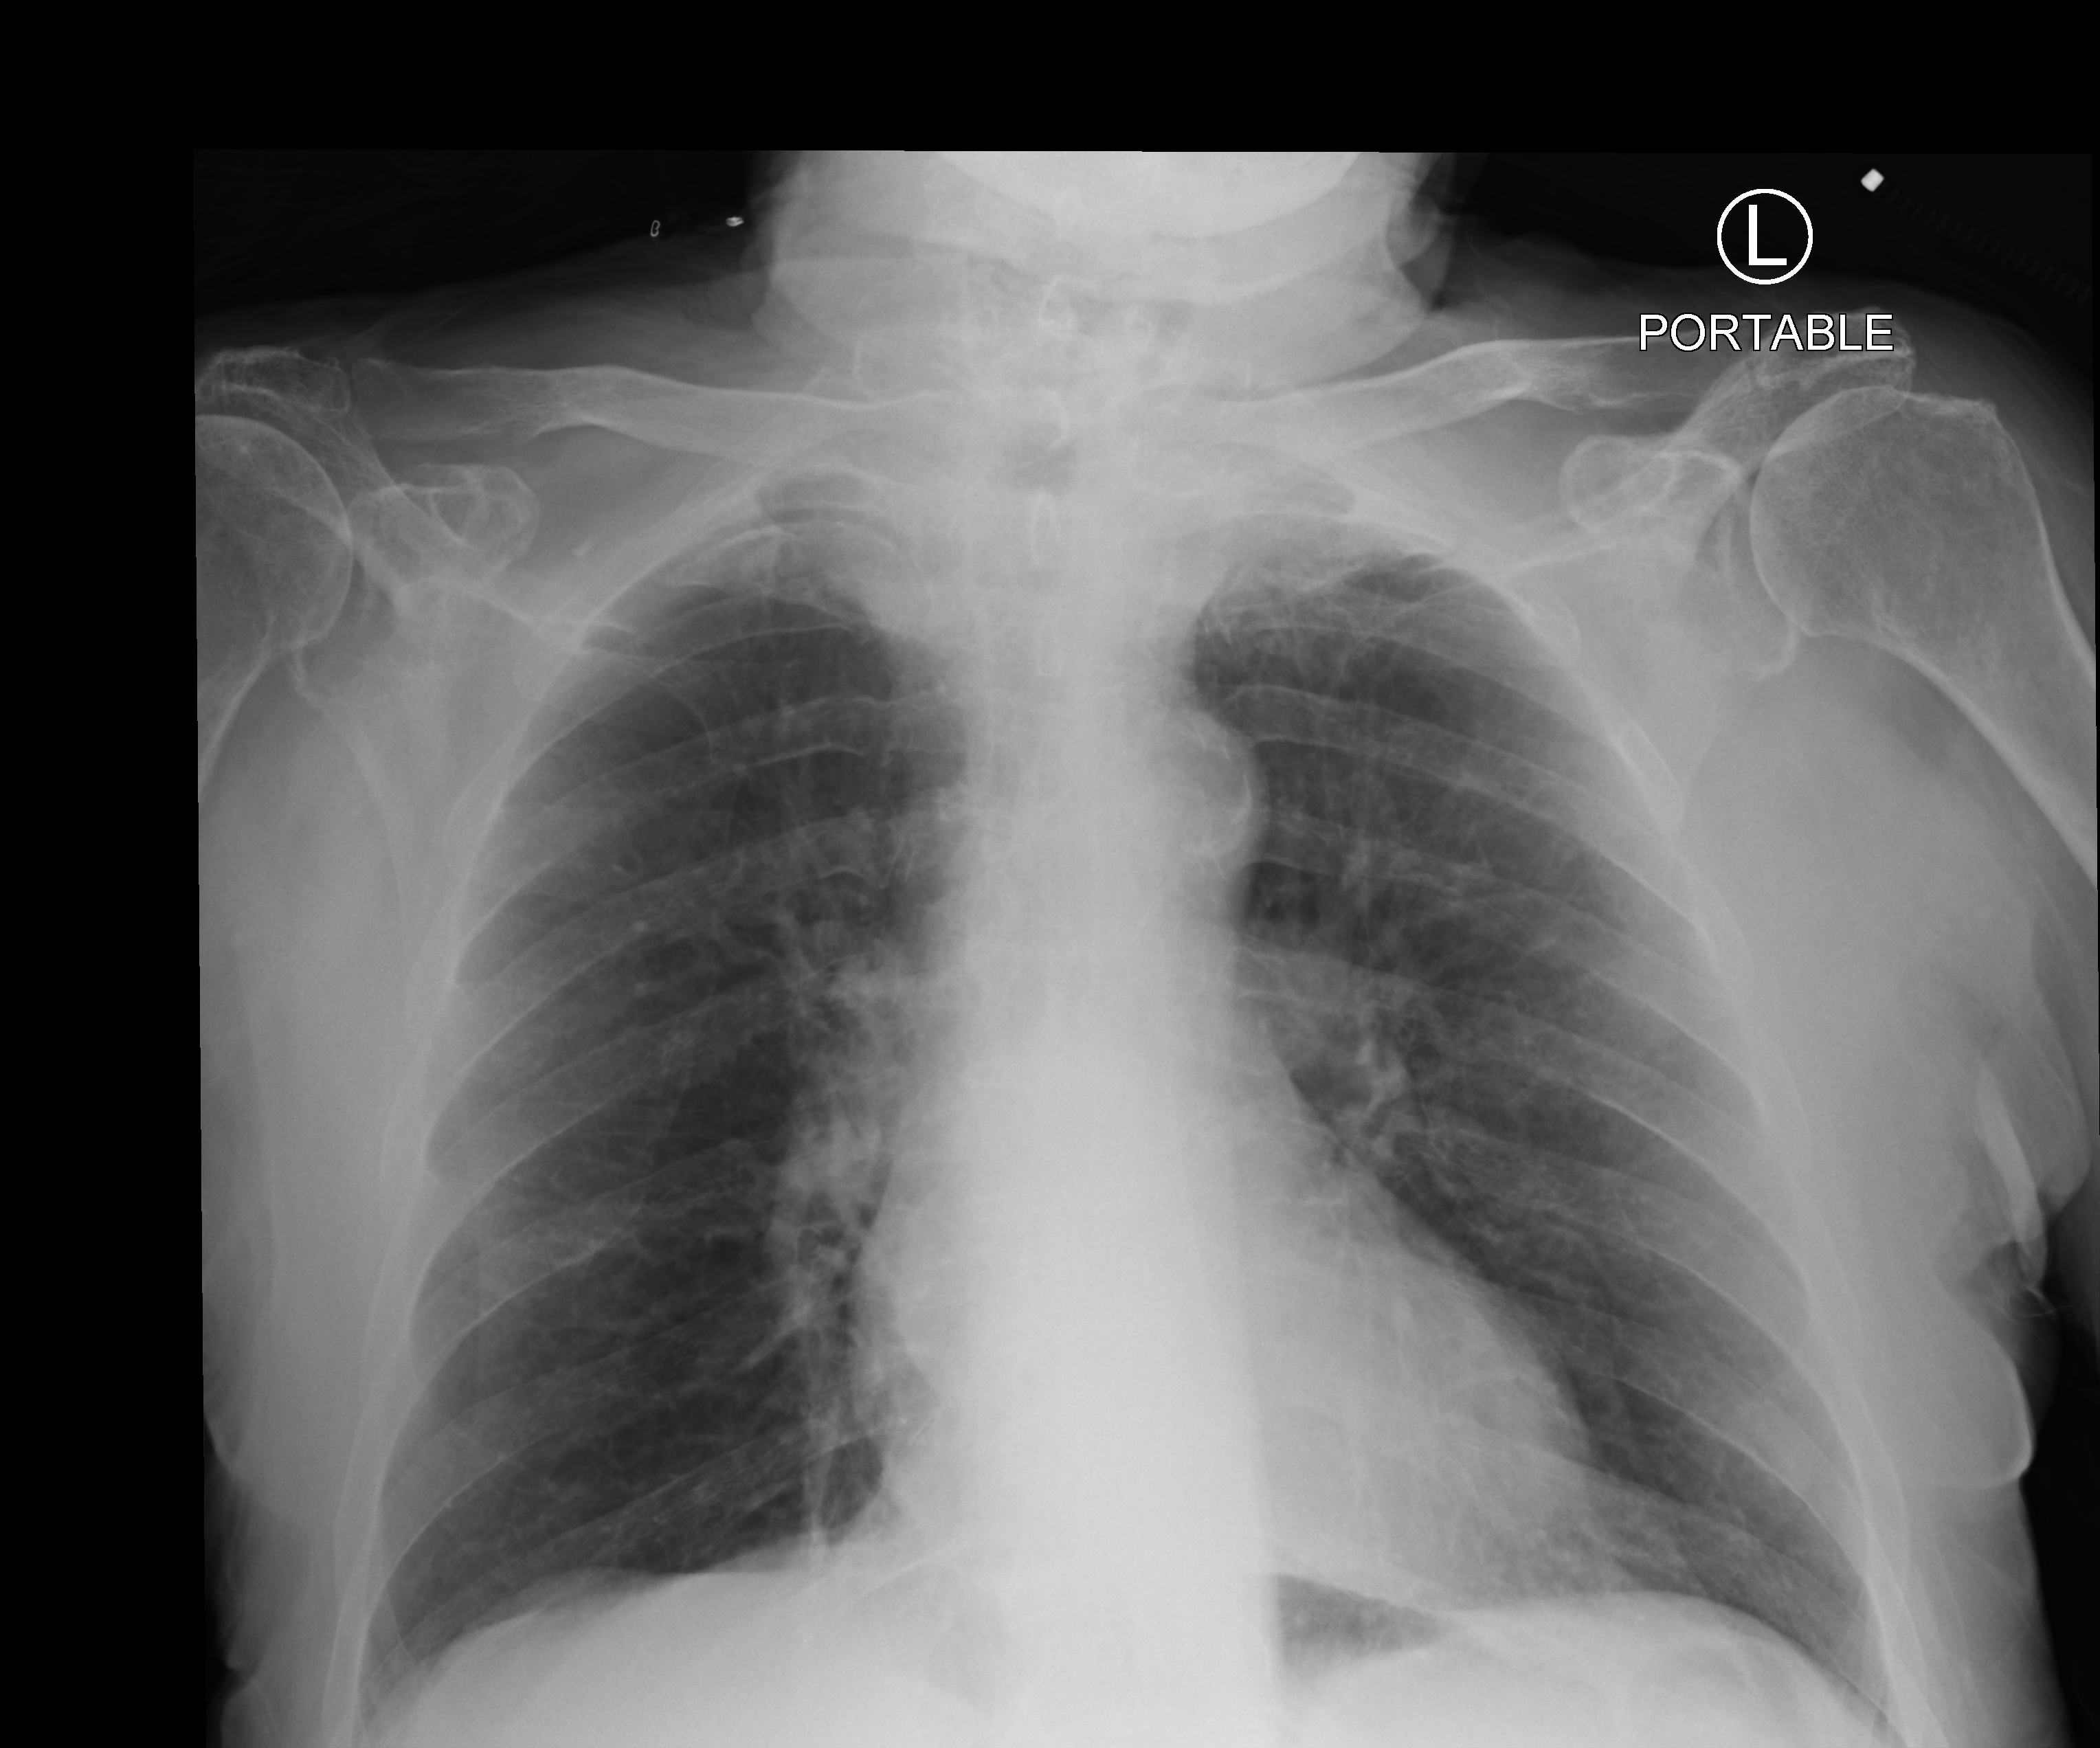
Chest X-ray (portable), anteroposterior (AP) projection. Male patient hospitalised with COVID-19, age 75–90 years.
Admission-level facts for this patient (not findings on this image; timing relative to this image not recorded): admitted to intensive care during this hospital stay: no; other chronic lung disease (admission record): no; mechanically ventilated during this hospital stay: no.